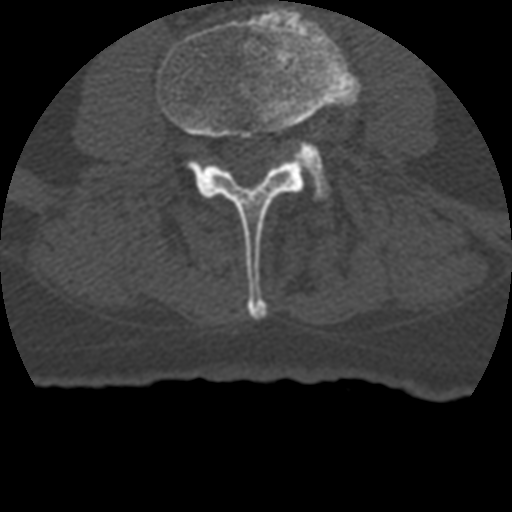
CT including the spine, one axial slice. Position 85 of 399 along the scan axis. Bone window (W 1800 / L 400 HU). 512 × 512 image matrix, field of view 160 × 160 mm. Patient age 69 years. Case-level facts recorded for this patient, not image findings: primary cancer: prostate.
Annotated regions visible in this slice (semi-automatic segmentation, software-assisted and operator-edited):
- L3 vertebra: bounding box <157,7,355,319> (left, top, right, bottom; pixels)
- L4 vertebra: <295,144,329,199>